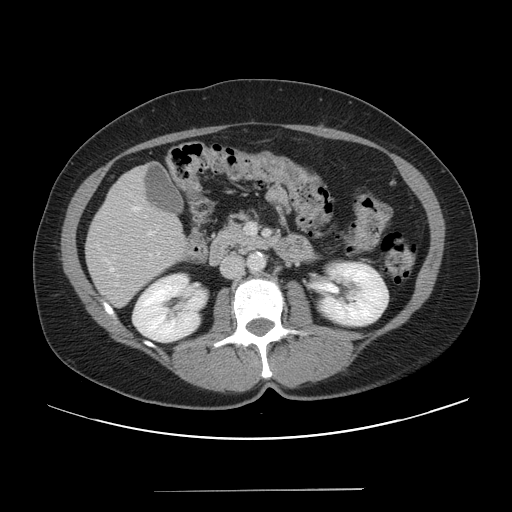
Contrast-enhanced abdominal CT, one axial slice. Position 17 of 56 along the scan axis. Intravenous contrast given. Soft-tissue window (W 400 / L 40 HU). 5 mm slice thickness. 512 × 512 image matrix. Female patient, age 54 years. Case-level facts recorded for this patient, not image findings: diagnosis: colorectal cancer liver metastases, imaged before liver resection; multiple liver metastases: yes; largest metastasis: 3.2 cm.
Outlined on this slice (outlined manually by an expert reader):
- hepatic veins: bounding box [x1, y1, x2, y2] px = [110, 268, 113, 271]
- liver: [87, 166, 188, 307]
- portal vein (with intrahepatic branches): [148, 225, 255, 235]